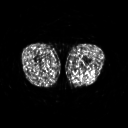
FDG PET of an extremity soft-tissue mass (from a PET/CT study), one axial slice. Position 210 of 267 along the scan axis. 3.27 mm slice thickness. 128 × 128 image matrix. Patient: male, 27 years. Case-level facts recorded for this patient, not image findings: histological type: extraskeletal osteosarcoma; grade: high; site of the primary tumour: left adductur.
Outlined on this slice (expert contour drawn on MRI and transferred to this co-registered scan by the dataset authors):
- gross tumour volume (mass): bounding box [x1, y1, x2, y2] px = [84, 65, 87, 67]